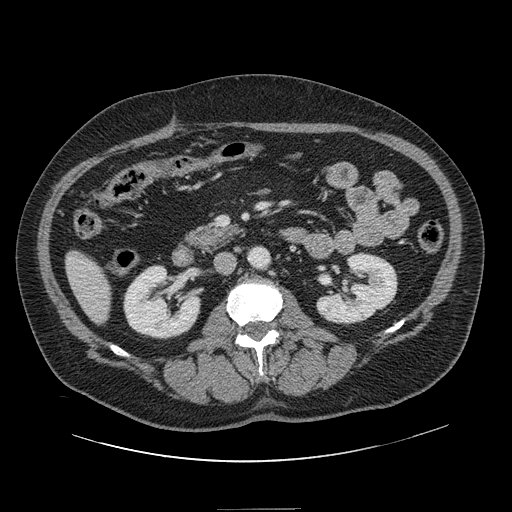
Contrast-enhanced abdominal CT, one axial slice. Position 41 of 154 along the scan axis. Intravenous contrast given. Soft-tissue window (W 400 / L 40 HU). 2.5 mm slice thickness. 512 × 512 image matrix, field of view 451 × 451 mm. Male patient, age 61 years. Case-level facts recorded for this patient, not image findings: diagnosis: colorectal cancer liver metastases, imaged before liver resection; multiple liver metastases: yes; largest metastasis: 2.6 cm; disease in both lobes: yes.
Outlined on this slice (manually delineated by an expert):
- liver: box from (x=67, y=252) to (x=110, y=323) px
- planned liver remnant (the part of the liver to remain after resection): (x=67, y=252)–(x=110, y=323)